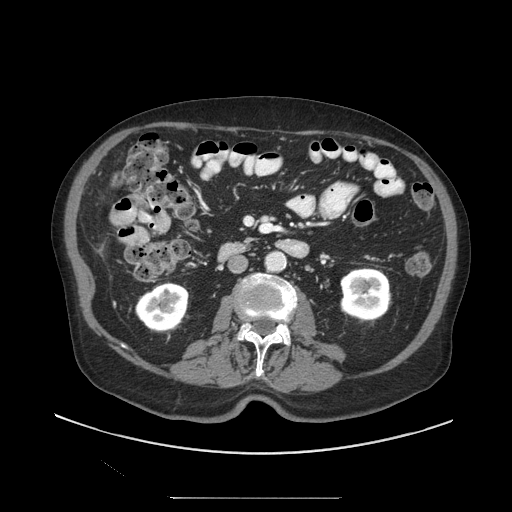
Contrast-enhanced abdominal CT (liver protocol), one axial slice. Position 27 of 97 along the scan axis. Reconstruction kernel STANDARD. Soft-tissue window (W 400 / L 40 HU). 512 × 512 image matrix. From the clinical record (not read from this slice): diagnosis: hepatocellular carcinoma (patient treated with transarterial chemoembolisation; whether this scan precedes or follows treatment is not stated here); TNM stage (as recorded): Stage-IIIC; Child-Pugh class: A; tumour nodularity: uninodular; tumour size: 9.2 cm.
Structures marked on this image (semi-automatically segmented with operator editing):
- liver parenchyma outside the tumour (the mass and vessels are separate outlines, so this box may not span the whole liver): bounding box <96,245,104,254> (left, top, right, bottom; pixels)